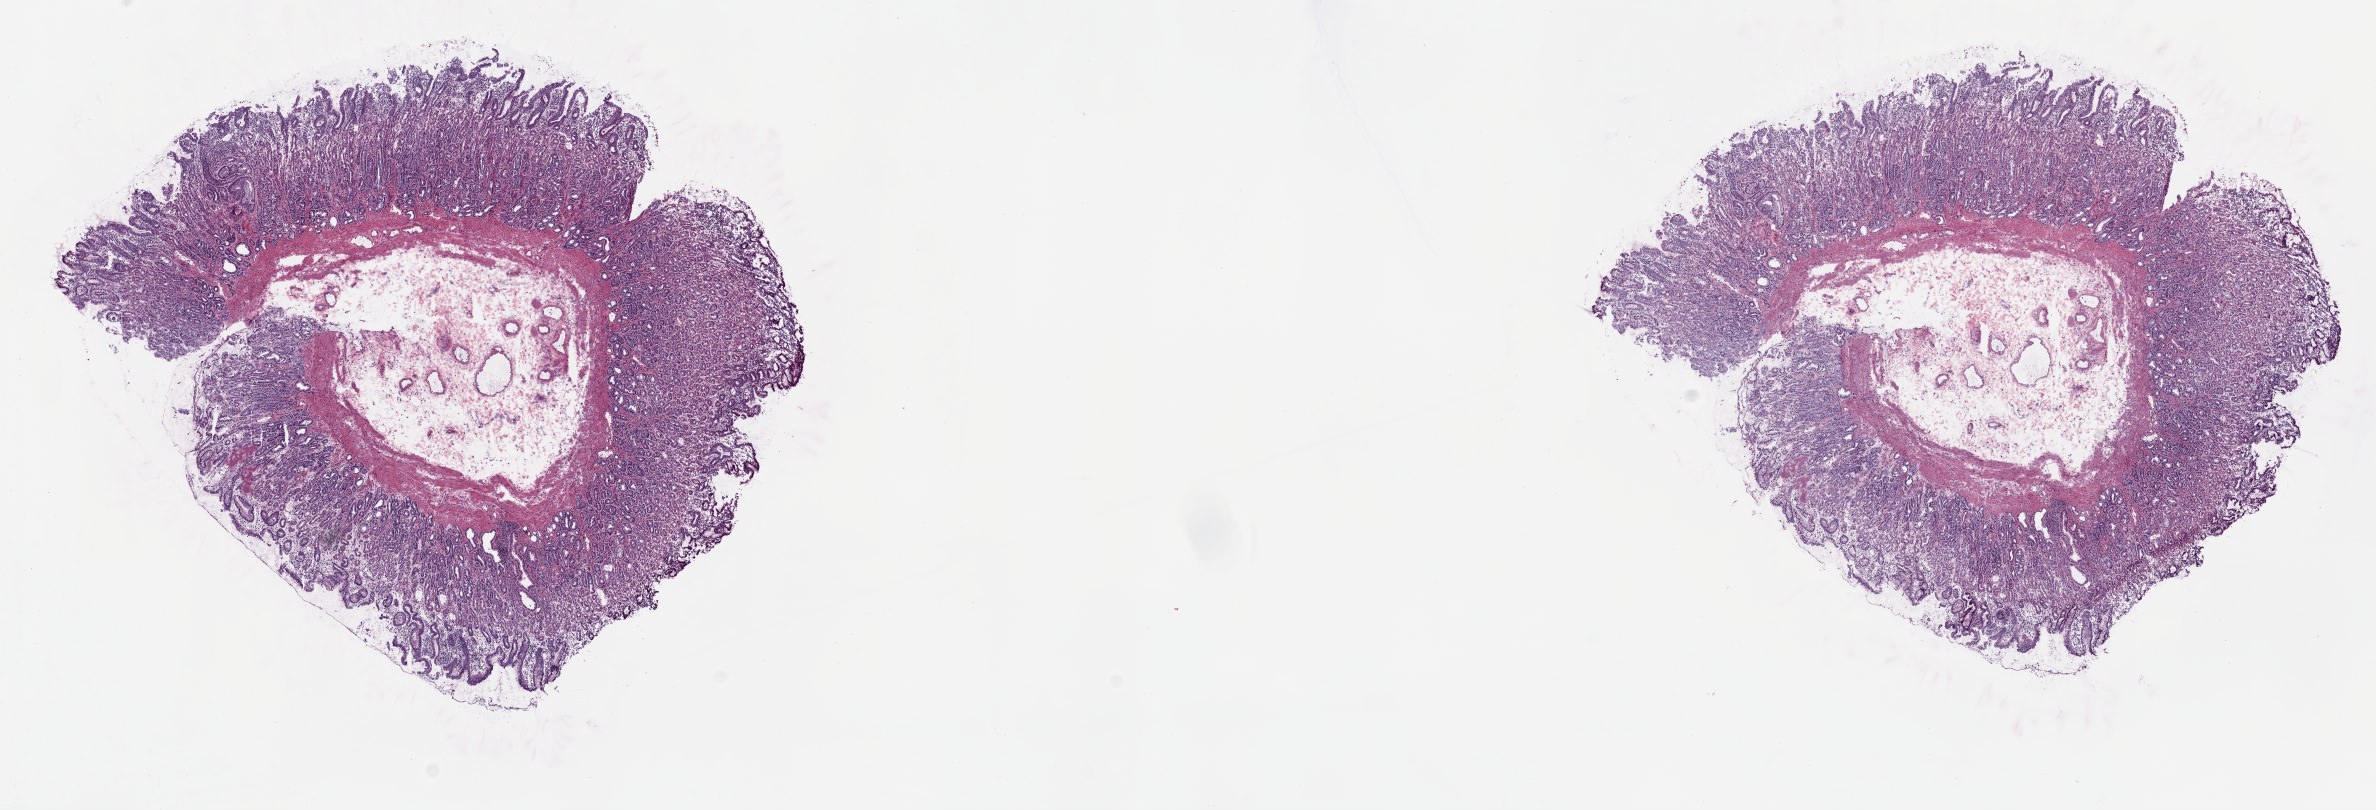
H&E-stained whole-slide image, shown as a low-resolution overview of the whole scanned area (about 18.8 x 6.4 mm), frozen section from the top of the tissue portion, sample: solid tissue normal (non-tumour tissue), esophagus. Female patient. Slide review estimates, as recorded: tumour cells 0%, tumour nuclei 0%, normal cells 100%, stromal cells 0%, necrosis 0%. Inflammatory infiltration, as recorded: lymphocyte infiltration 0%, monocyte infiltration 0%, neutrophil infiltration 0%.
This section: solid tissue normal sample (biorepository sample class). Patient diagnosis: Adenocarcinoma, NOS.